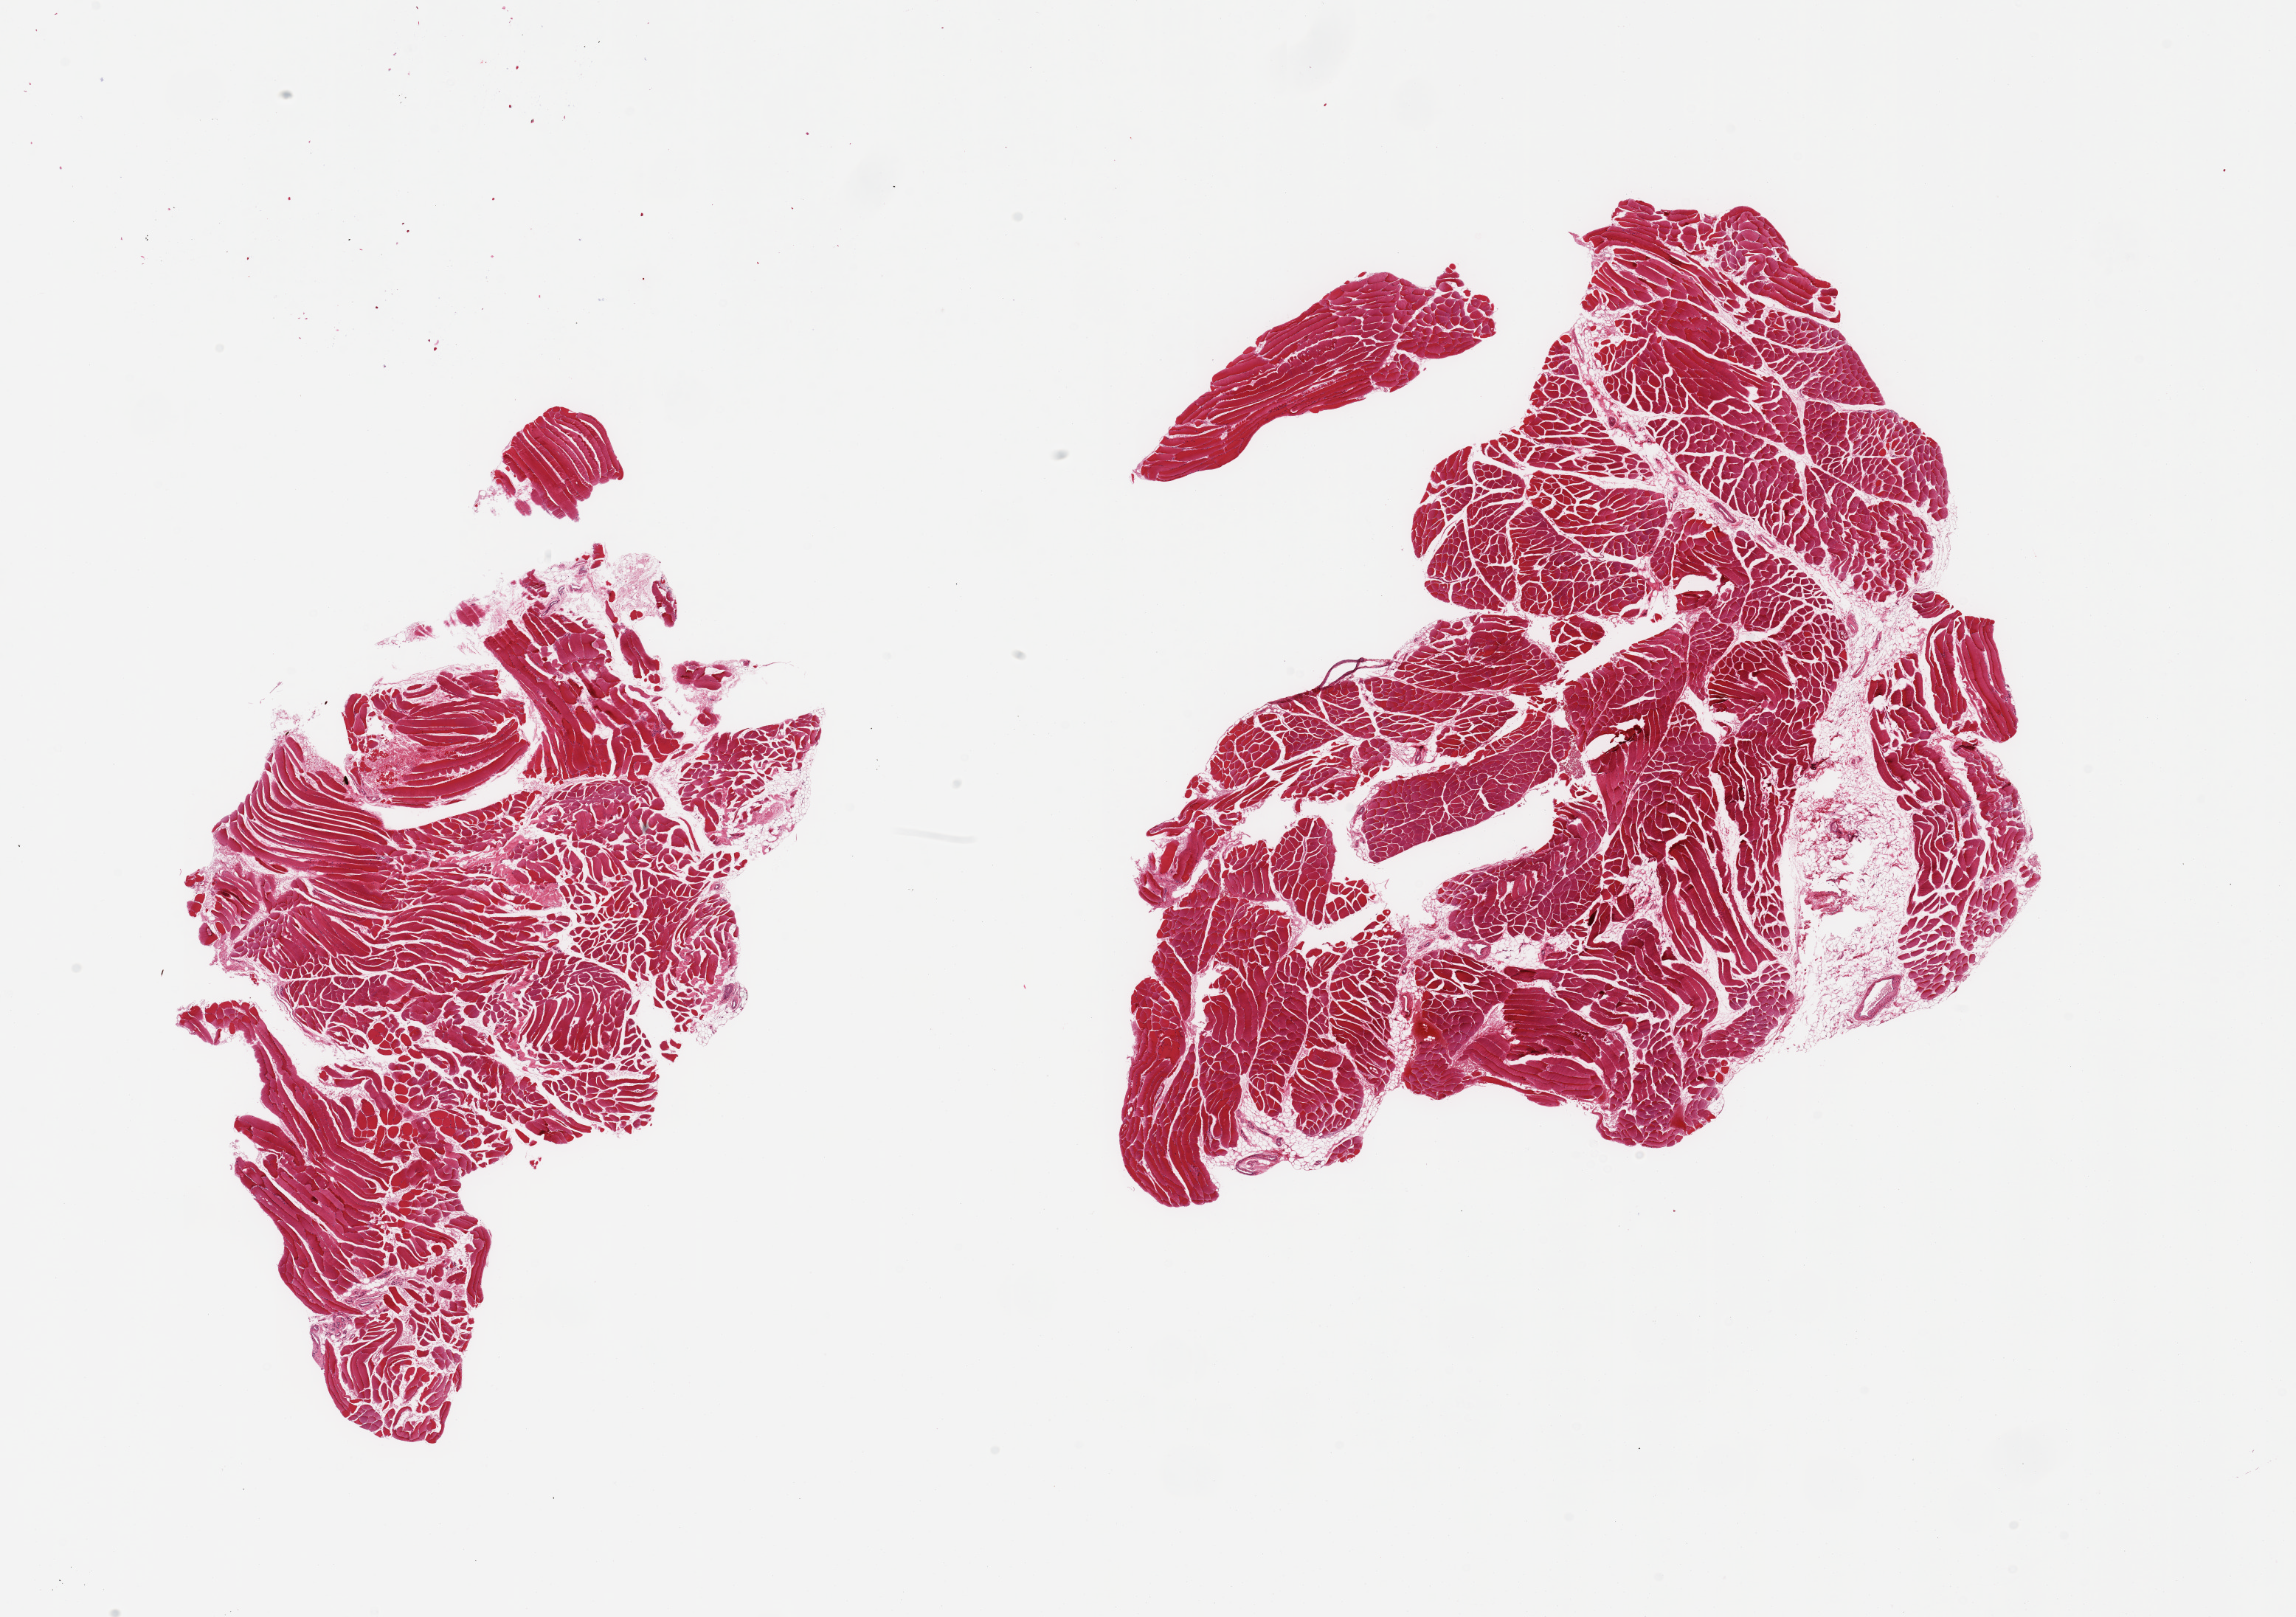
Haematoxylin and eosin whole-slide image — a low-resolution overview of the entire scanned area, about 24.6 x 17.3 mm (from a 20x scan), PAXgene-fixed paraffin-embedded (PFPE) section, target tissue: skeletal muscle, donor tissue sample. Male donor.
• review note (as recorded): 2 pieces; 10% internal fat